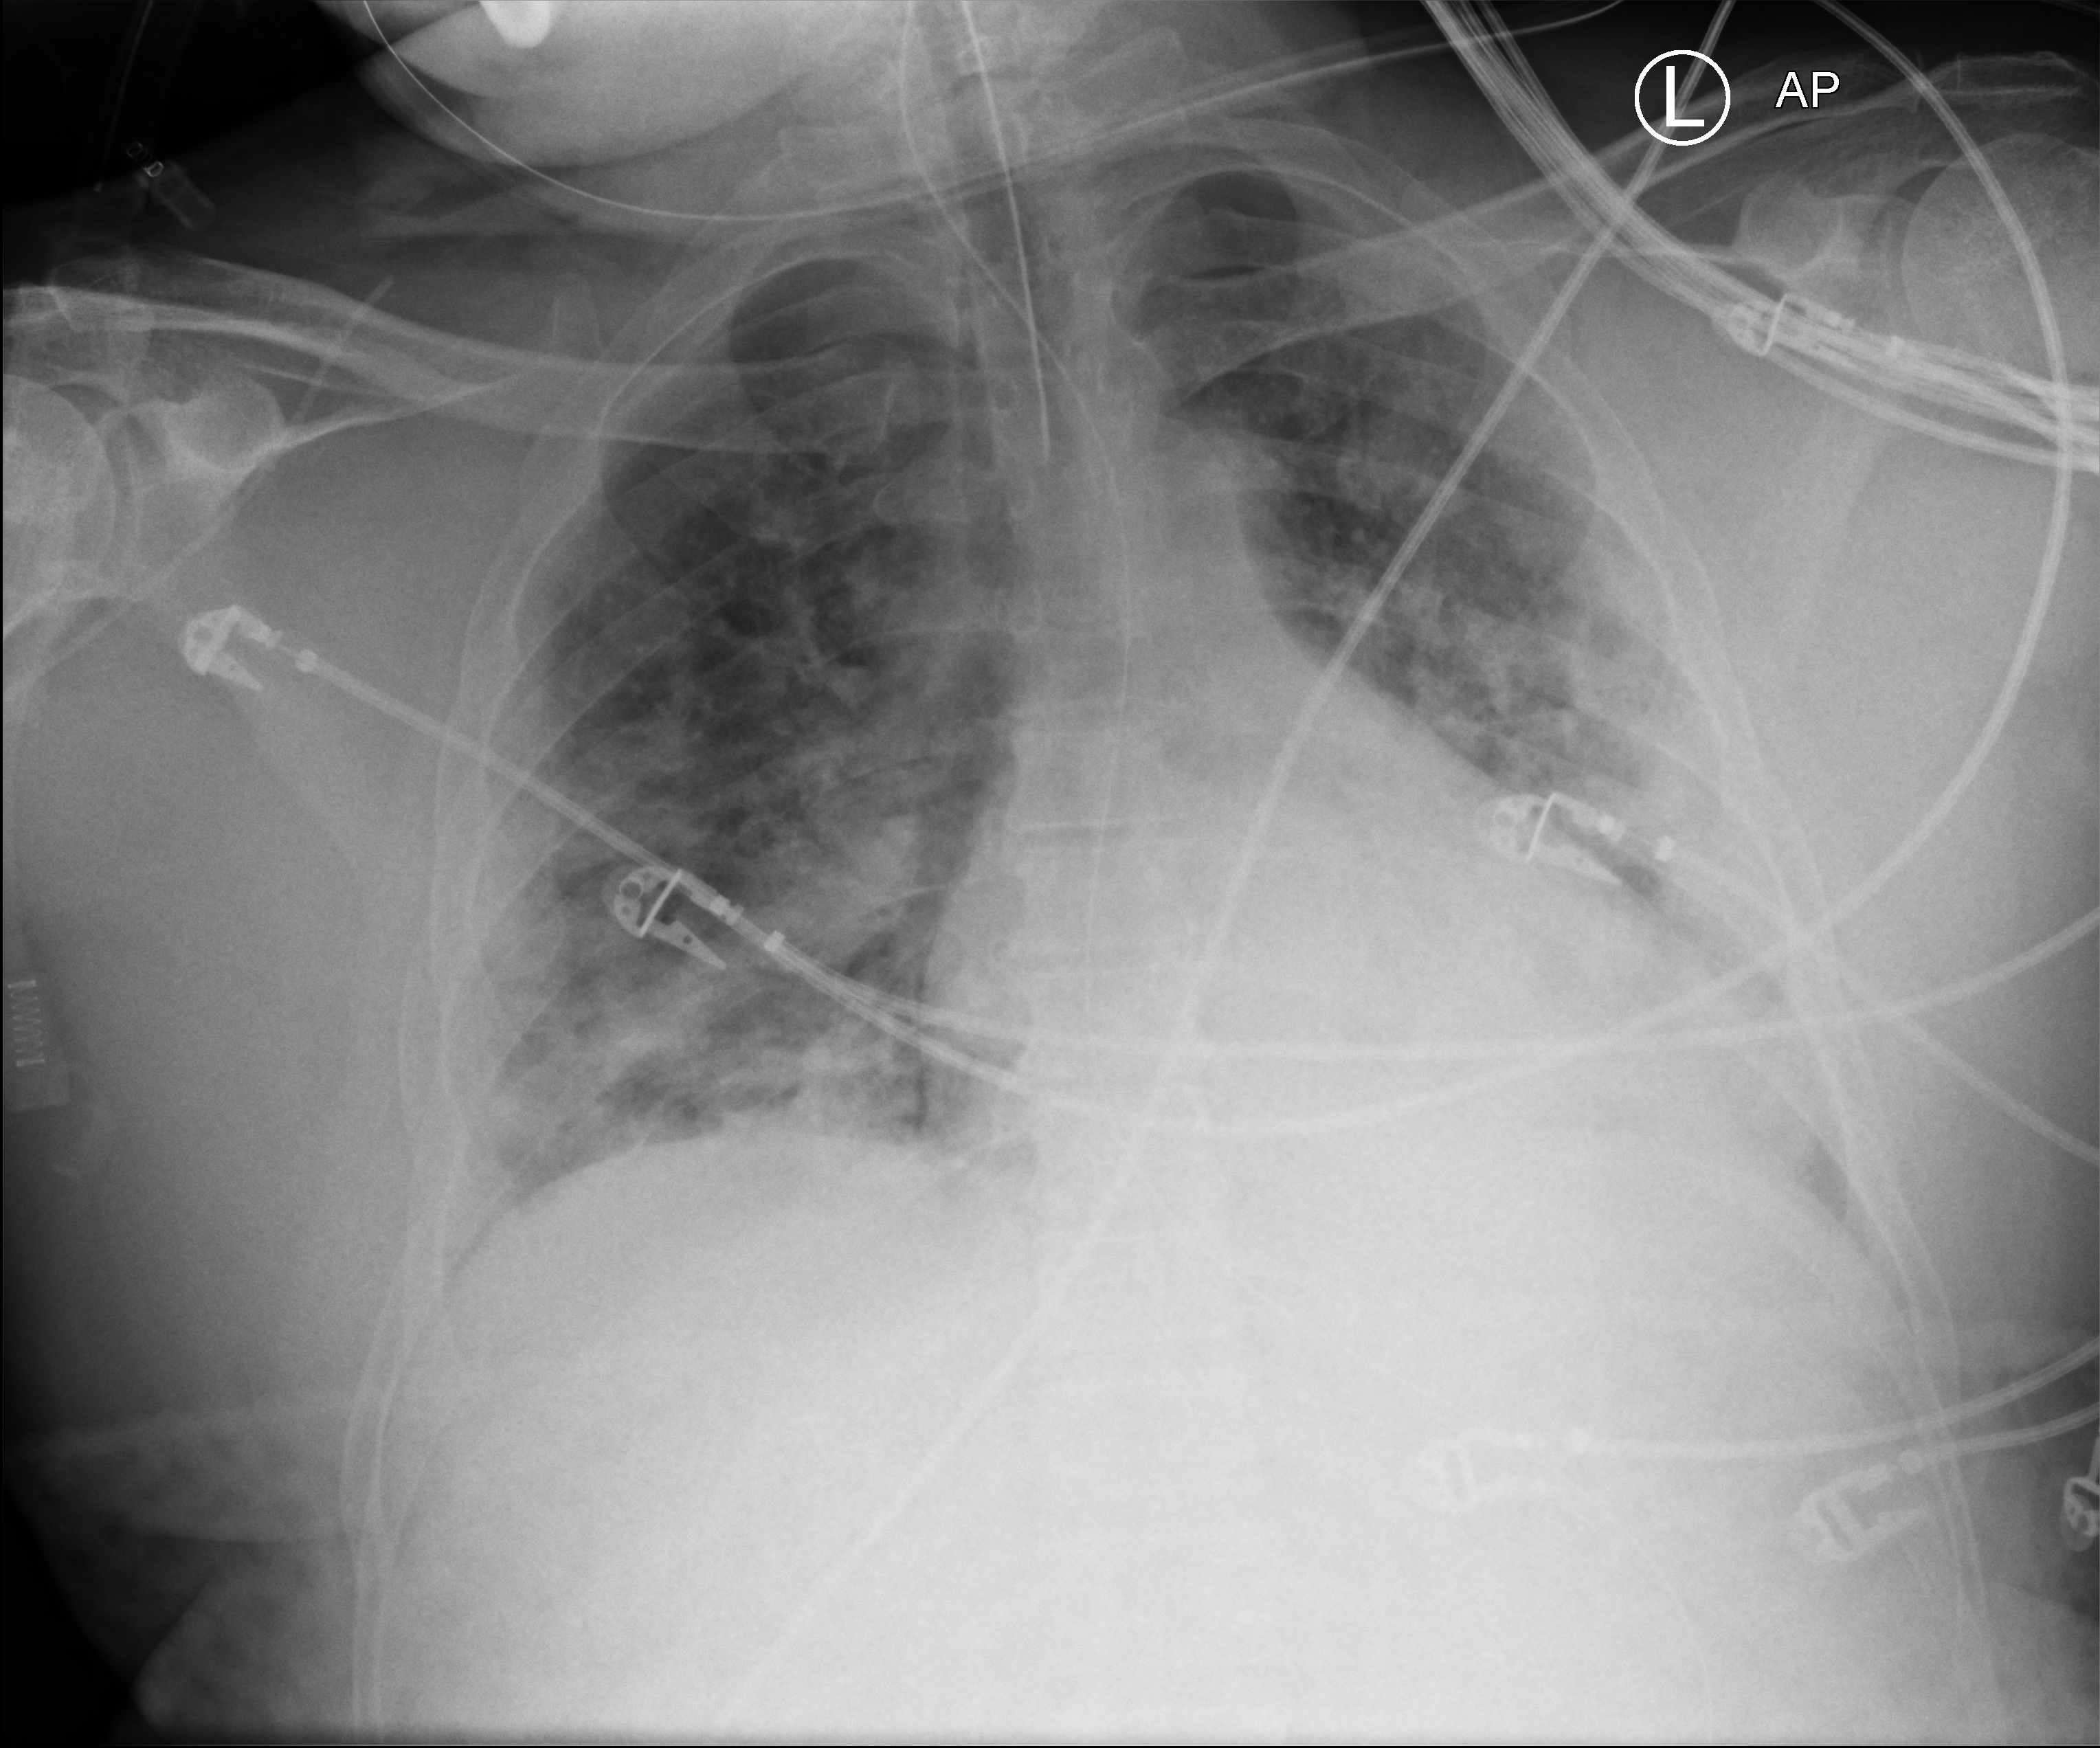
Bedside chest radiograph (computed radiography); anteroposterior (AP) projection. Male patient hospitalised with COVID-19, age 18–59 years.
Admission-level facts for this patient (not findings on this image; timing relative to this image not recorded): mechanically ventilated during this hospital stay: yes; length of hospital stay: 15 days; chronic kidney disease (admission record): no.